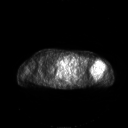
FDG PET of an extremity soft-tissue mass (from a PET/CT study), one axial slice. 3.27 mm slice thickness. 128 × 128 image matrix, field of view 700 × 700 mm. Patient: female, 83 years. From the clinical record (not read from this slice): histological type: pleiomorphic leiomyosarcoma; grade: high; site of the primary tumour: left biceps.
Annotated regions visible in this slice (expert contour drawn on MRI and transferred to this co-registered scan by the dataset authors):
- gross tumour volume including surrounding oedema: box from (x=90, y=59) to (x=106, y=77) px
- gross tumour volume (mass): (x=90, y=59)–(x=105, y=77)